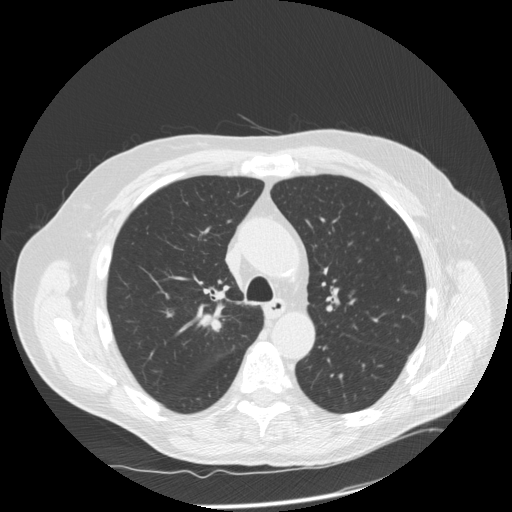
Low-dose screening chest CT, one axial slice; position 113 of 166 along the scan axis; reconstruction kernel STANDARD; 120 kVp; lung window (W 1500 / L -600 HU); 2.5 mm slice thickness; 512 × 512 image matrix, field of view 390 × 390 mm.
Structures marked on this image (manually delineated by an expert):
- lesion 1 (tumor, upper lobe of right lung): box from (x=200, y=315) to (x=220, y=330) px